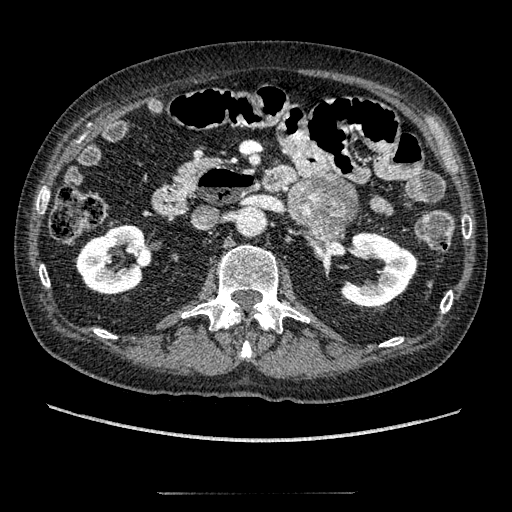
Contrast-enhanced abdominal CT, one axial slice; slice 91 of 274 in the series (ordered by position); reconstruction kernel STANDARD; 120 kVp; intravenous contrast given; soft-tissue window (W 400 / L 40 HU); 512 × 512 image matrix, field of view 381 × 381 mm. Male patient, age 69 years. From the clinical record (not read from this slice): diagnosis: adrenocortical carcinoma; tumour side: left adrenal; tumour size at pathology: 6.1 cm; Ki-67 index: 10 %; stage (as recorded): 3.
Outlined on this slice (semi-automatically segmented with operator editing):
- mass: bounding box (x1, y1, x2, y2) in pixels: (290, 178, 356, 237)